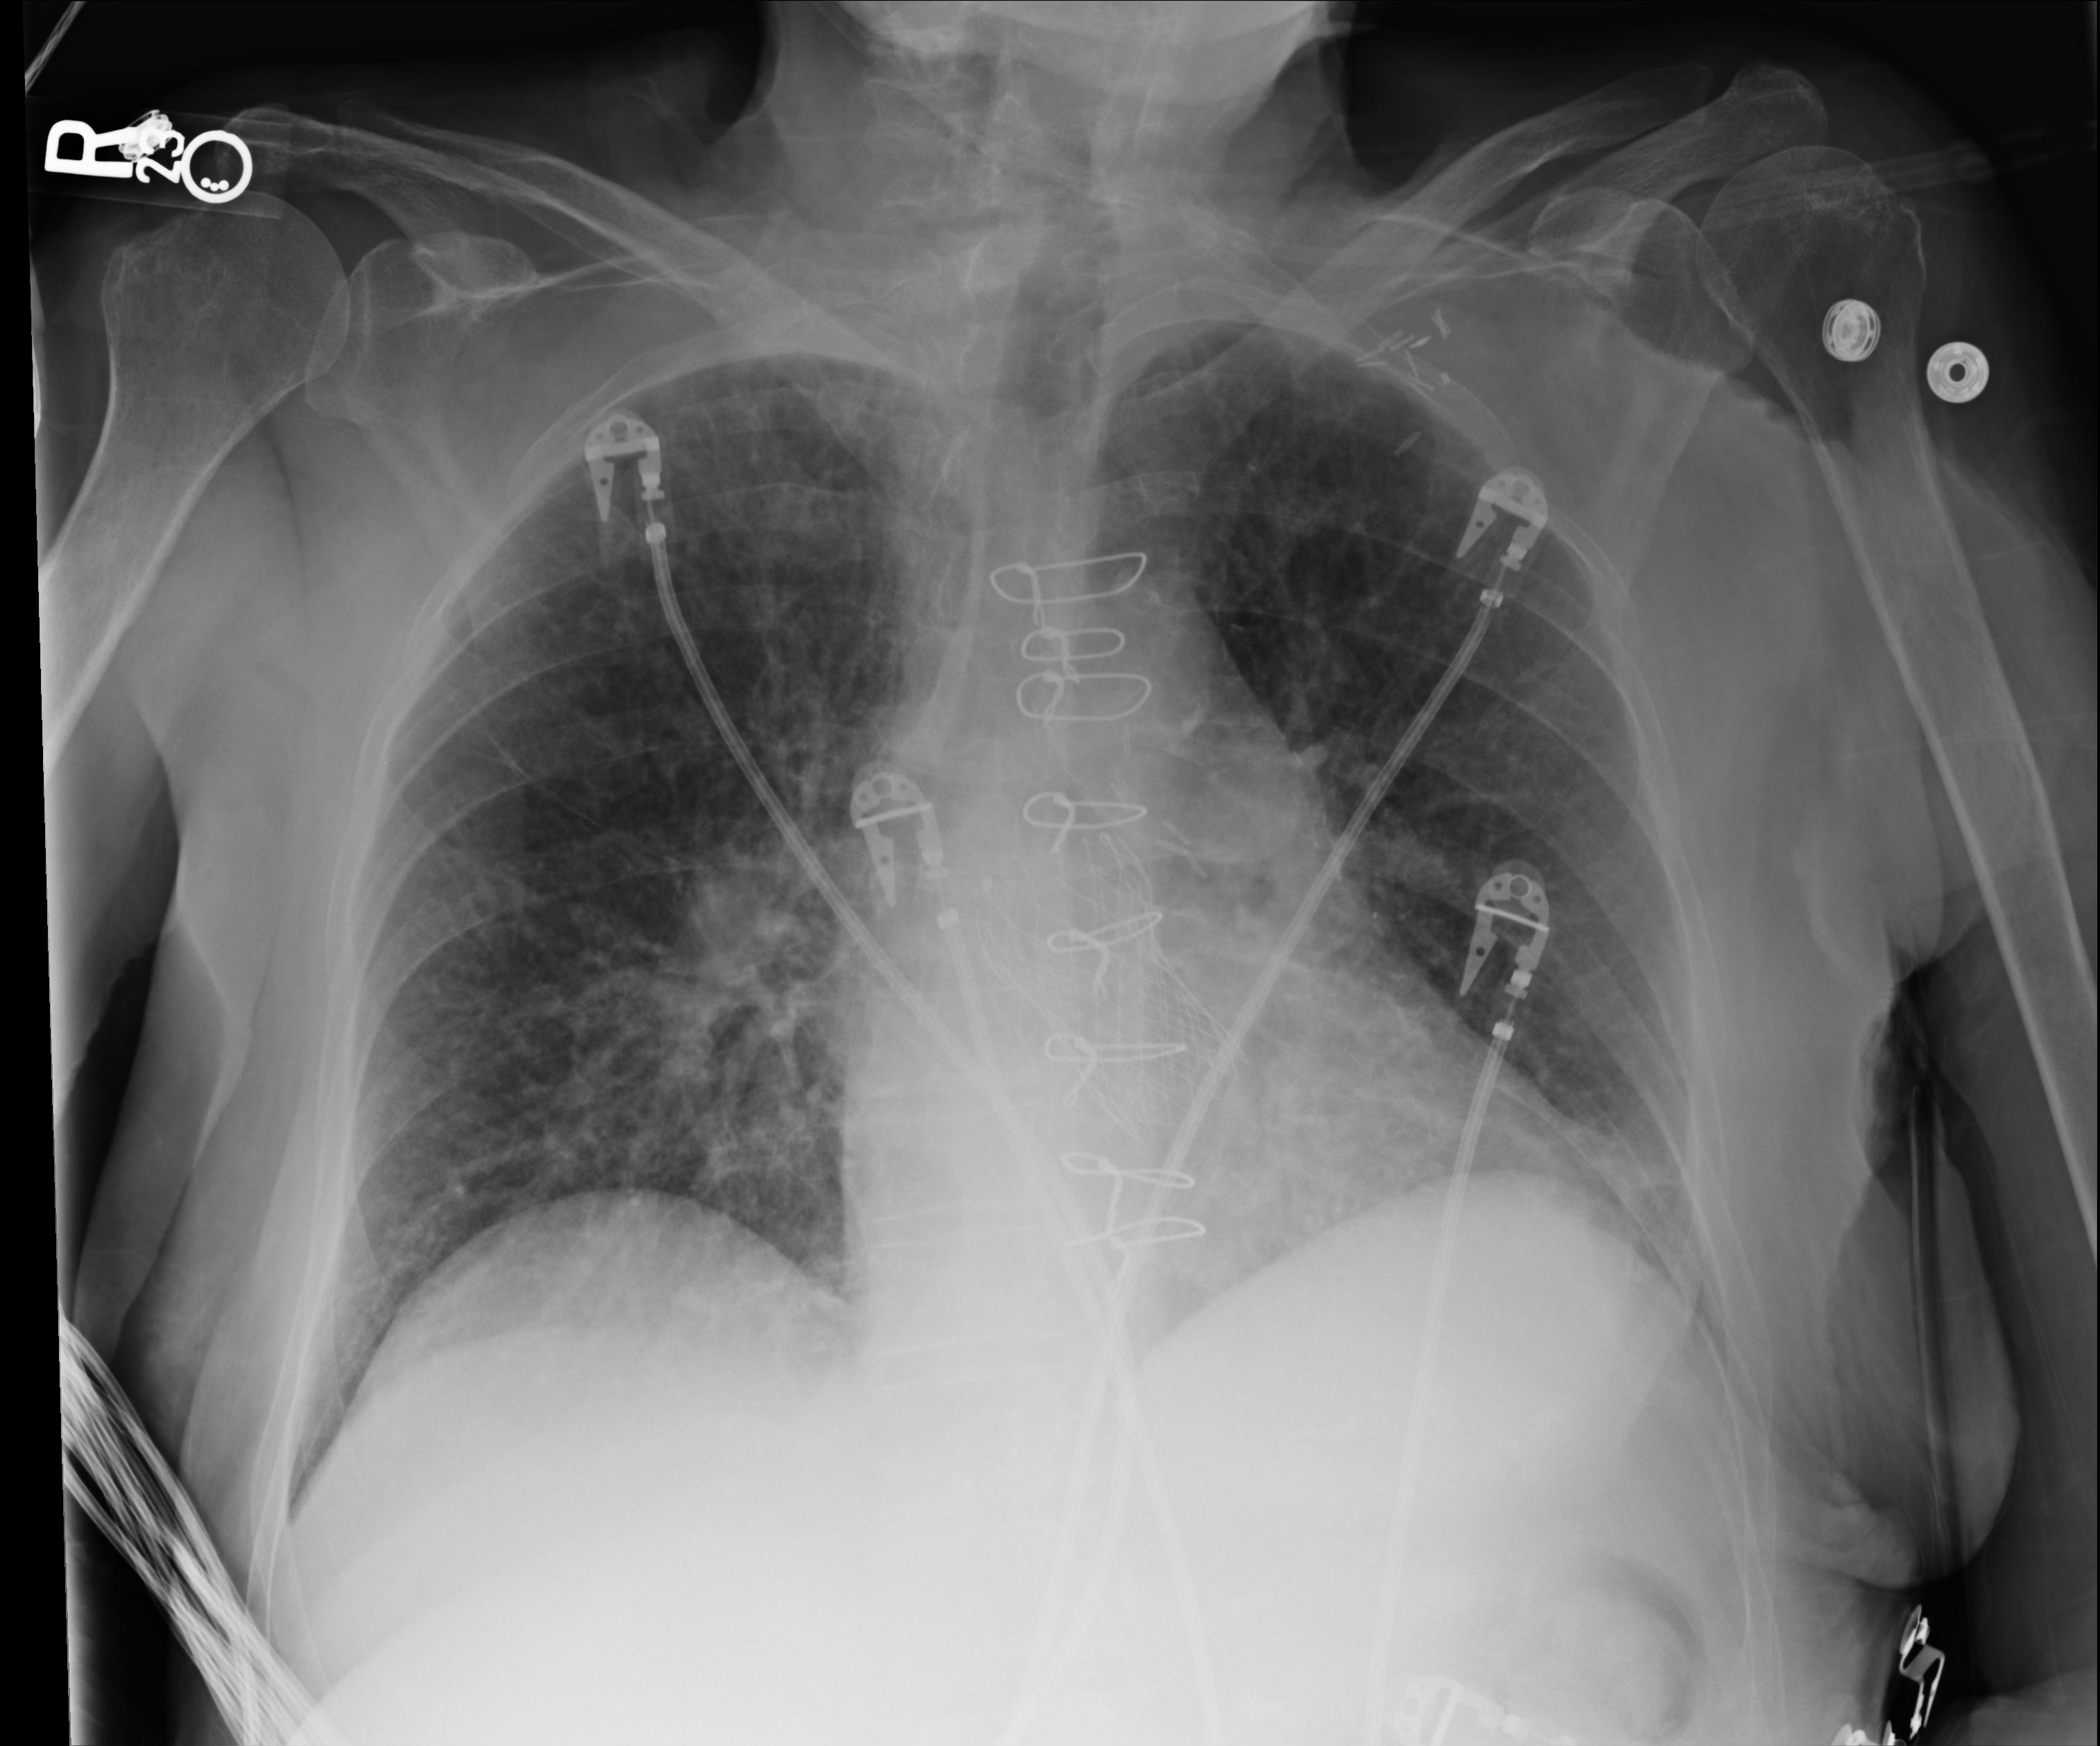
Bedside chest radiograph (computed radiography); anteroposterior (AP) projection. Female patient hospitalised with COVID-19, age 75–90 years.
Admission-level facts for this patient (not findings on this image; timing relative to this image not recorded):
- COPD (admission record): yes
- chronic kidney disease (admission record): no
- mechanically ventilated during this hospital stay: no